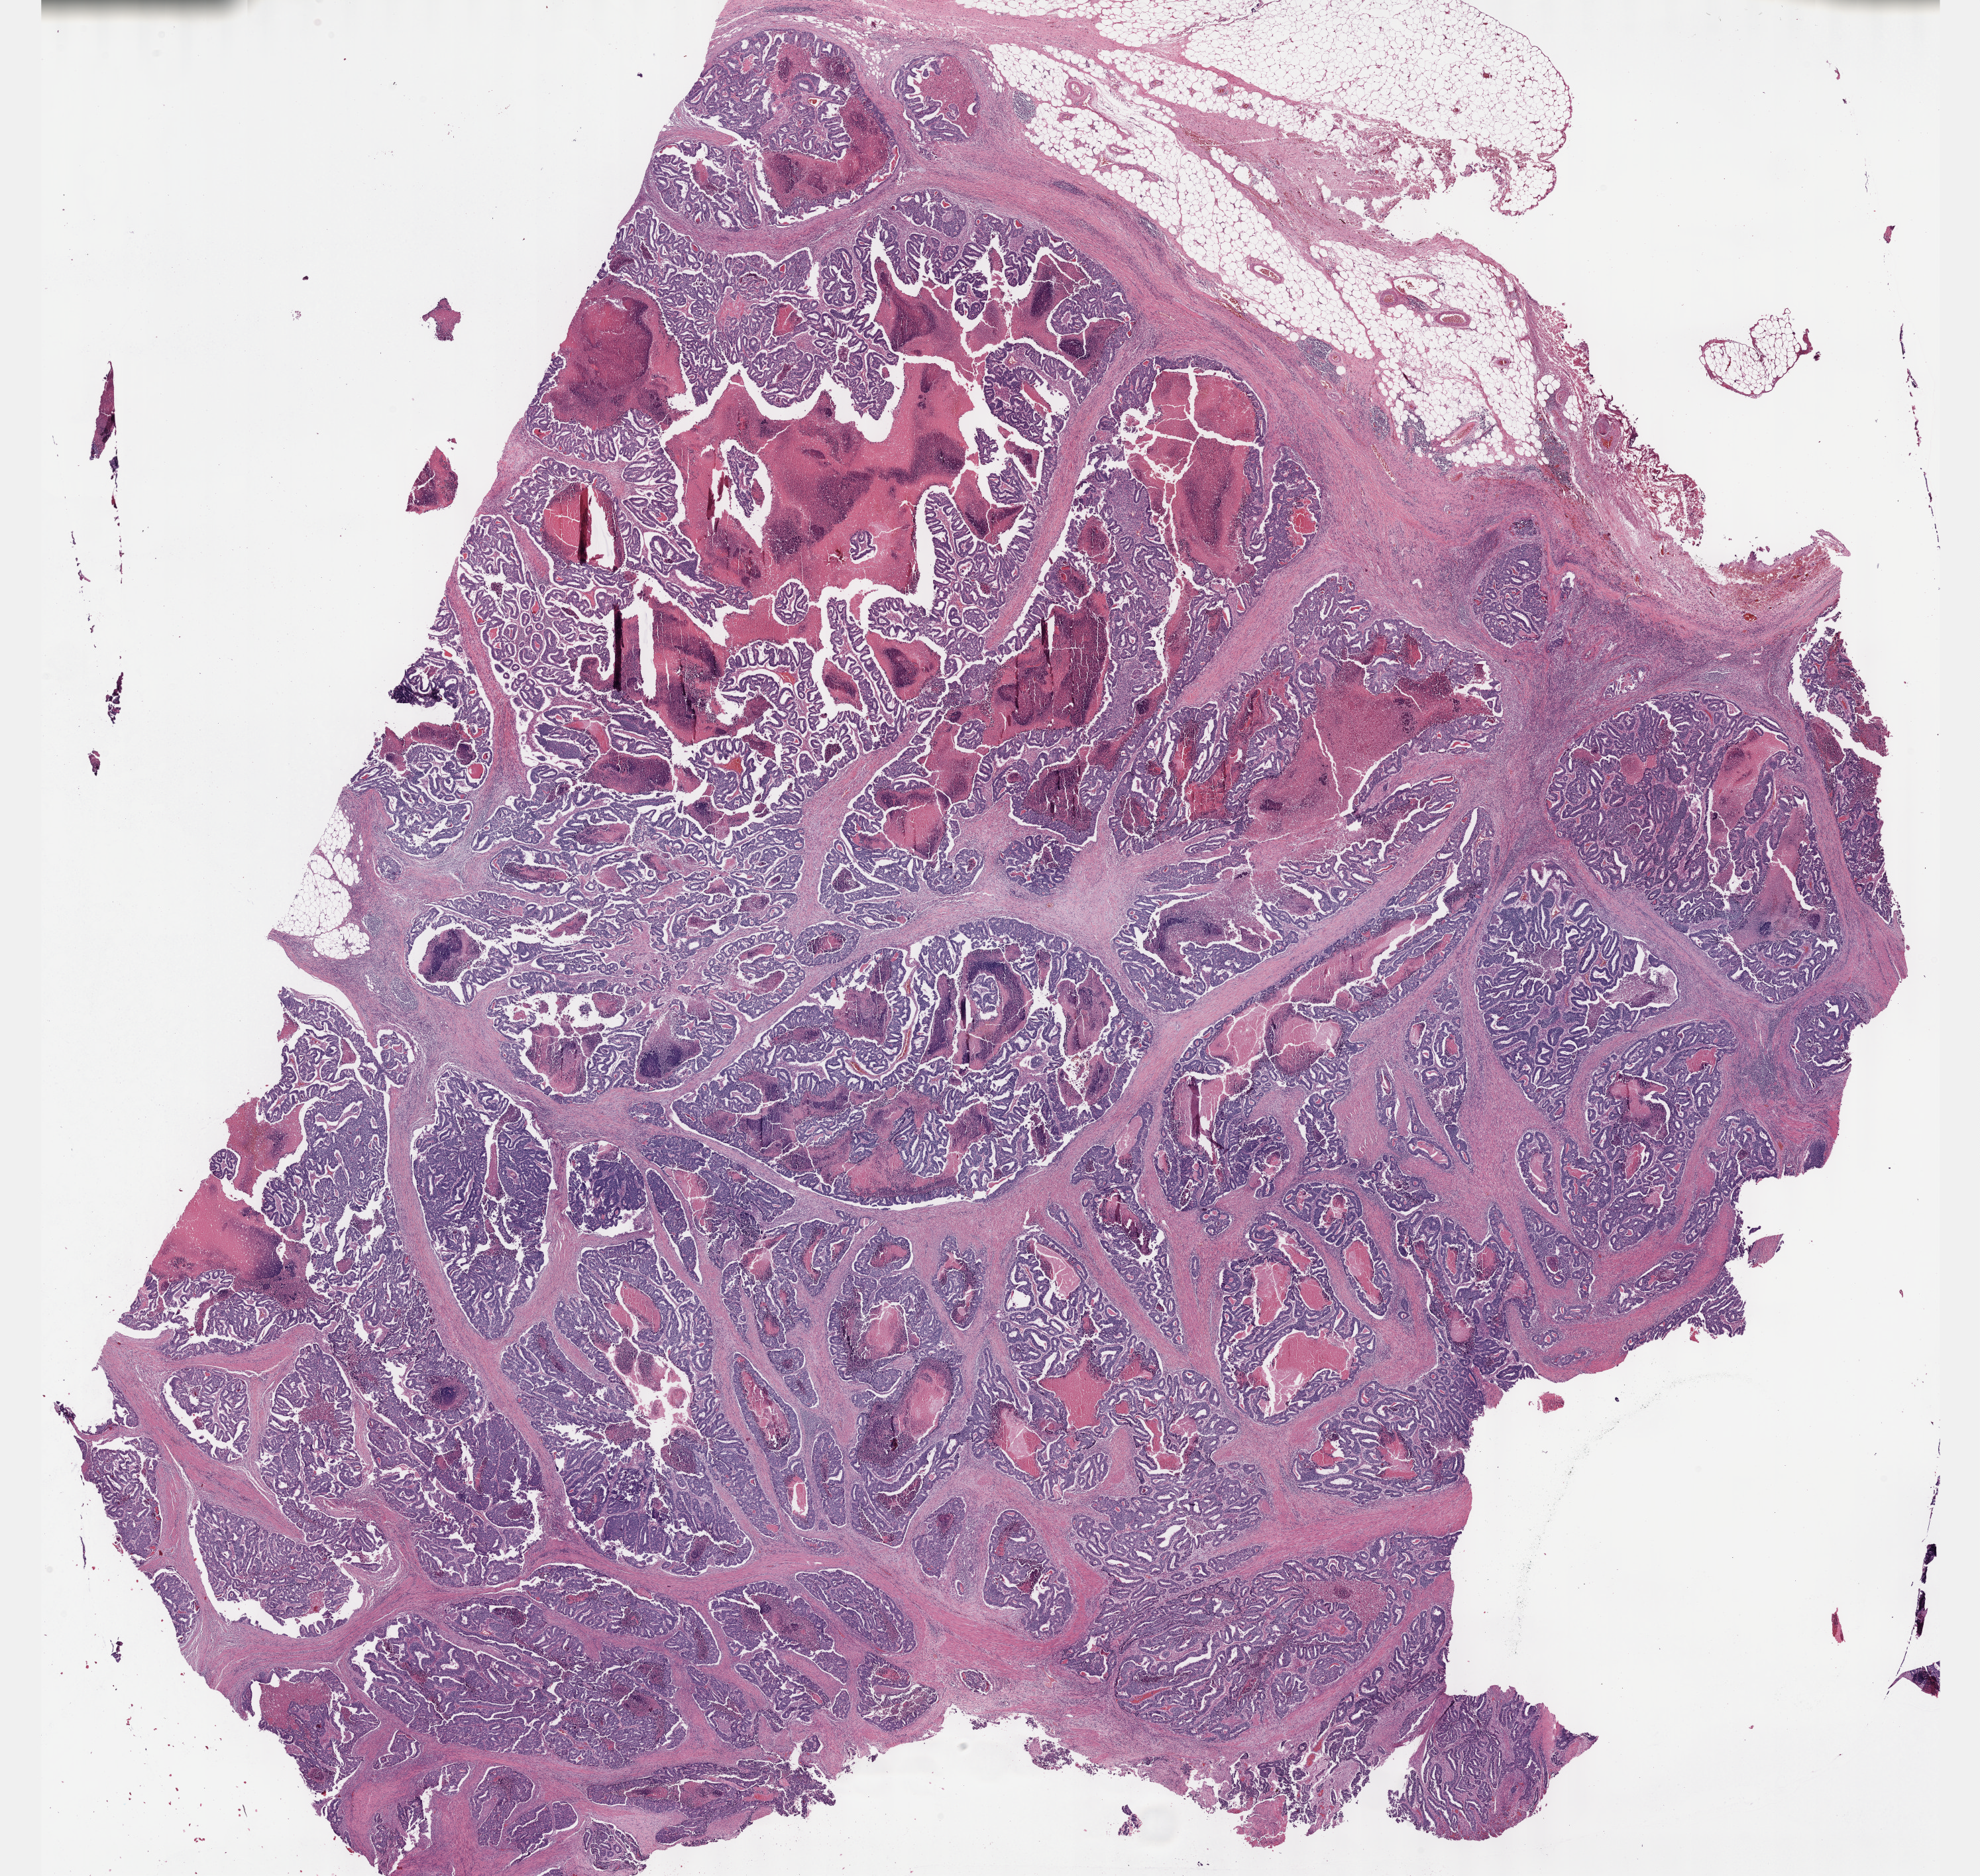
H&E whole-slide image — low-resolution overview of the scanned area, about 24.1 x 22.9 mm (acquisition: 40x scan). Formalin-fixed paraffin-embedded (FFPE) diagnostic section. Primary tumour sample from the stomach. Male, age 57 years at initial diagnosis. Histologic grade: G2 (moderately differentiated).
Histologic diagnosis: Tubular adenocarcinoma (body of stomach). AJCC pathologic stage: IIIB (6th edition). TNM: T3 N2 M0.